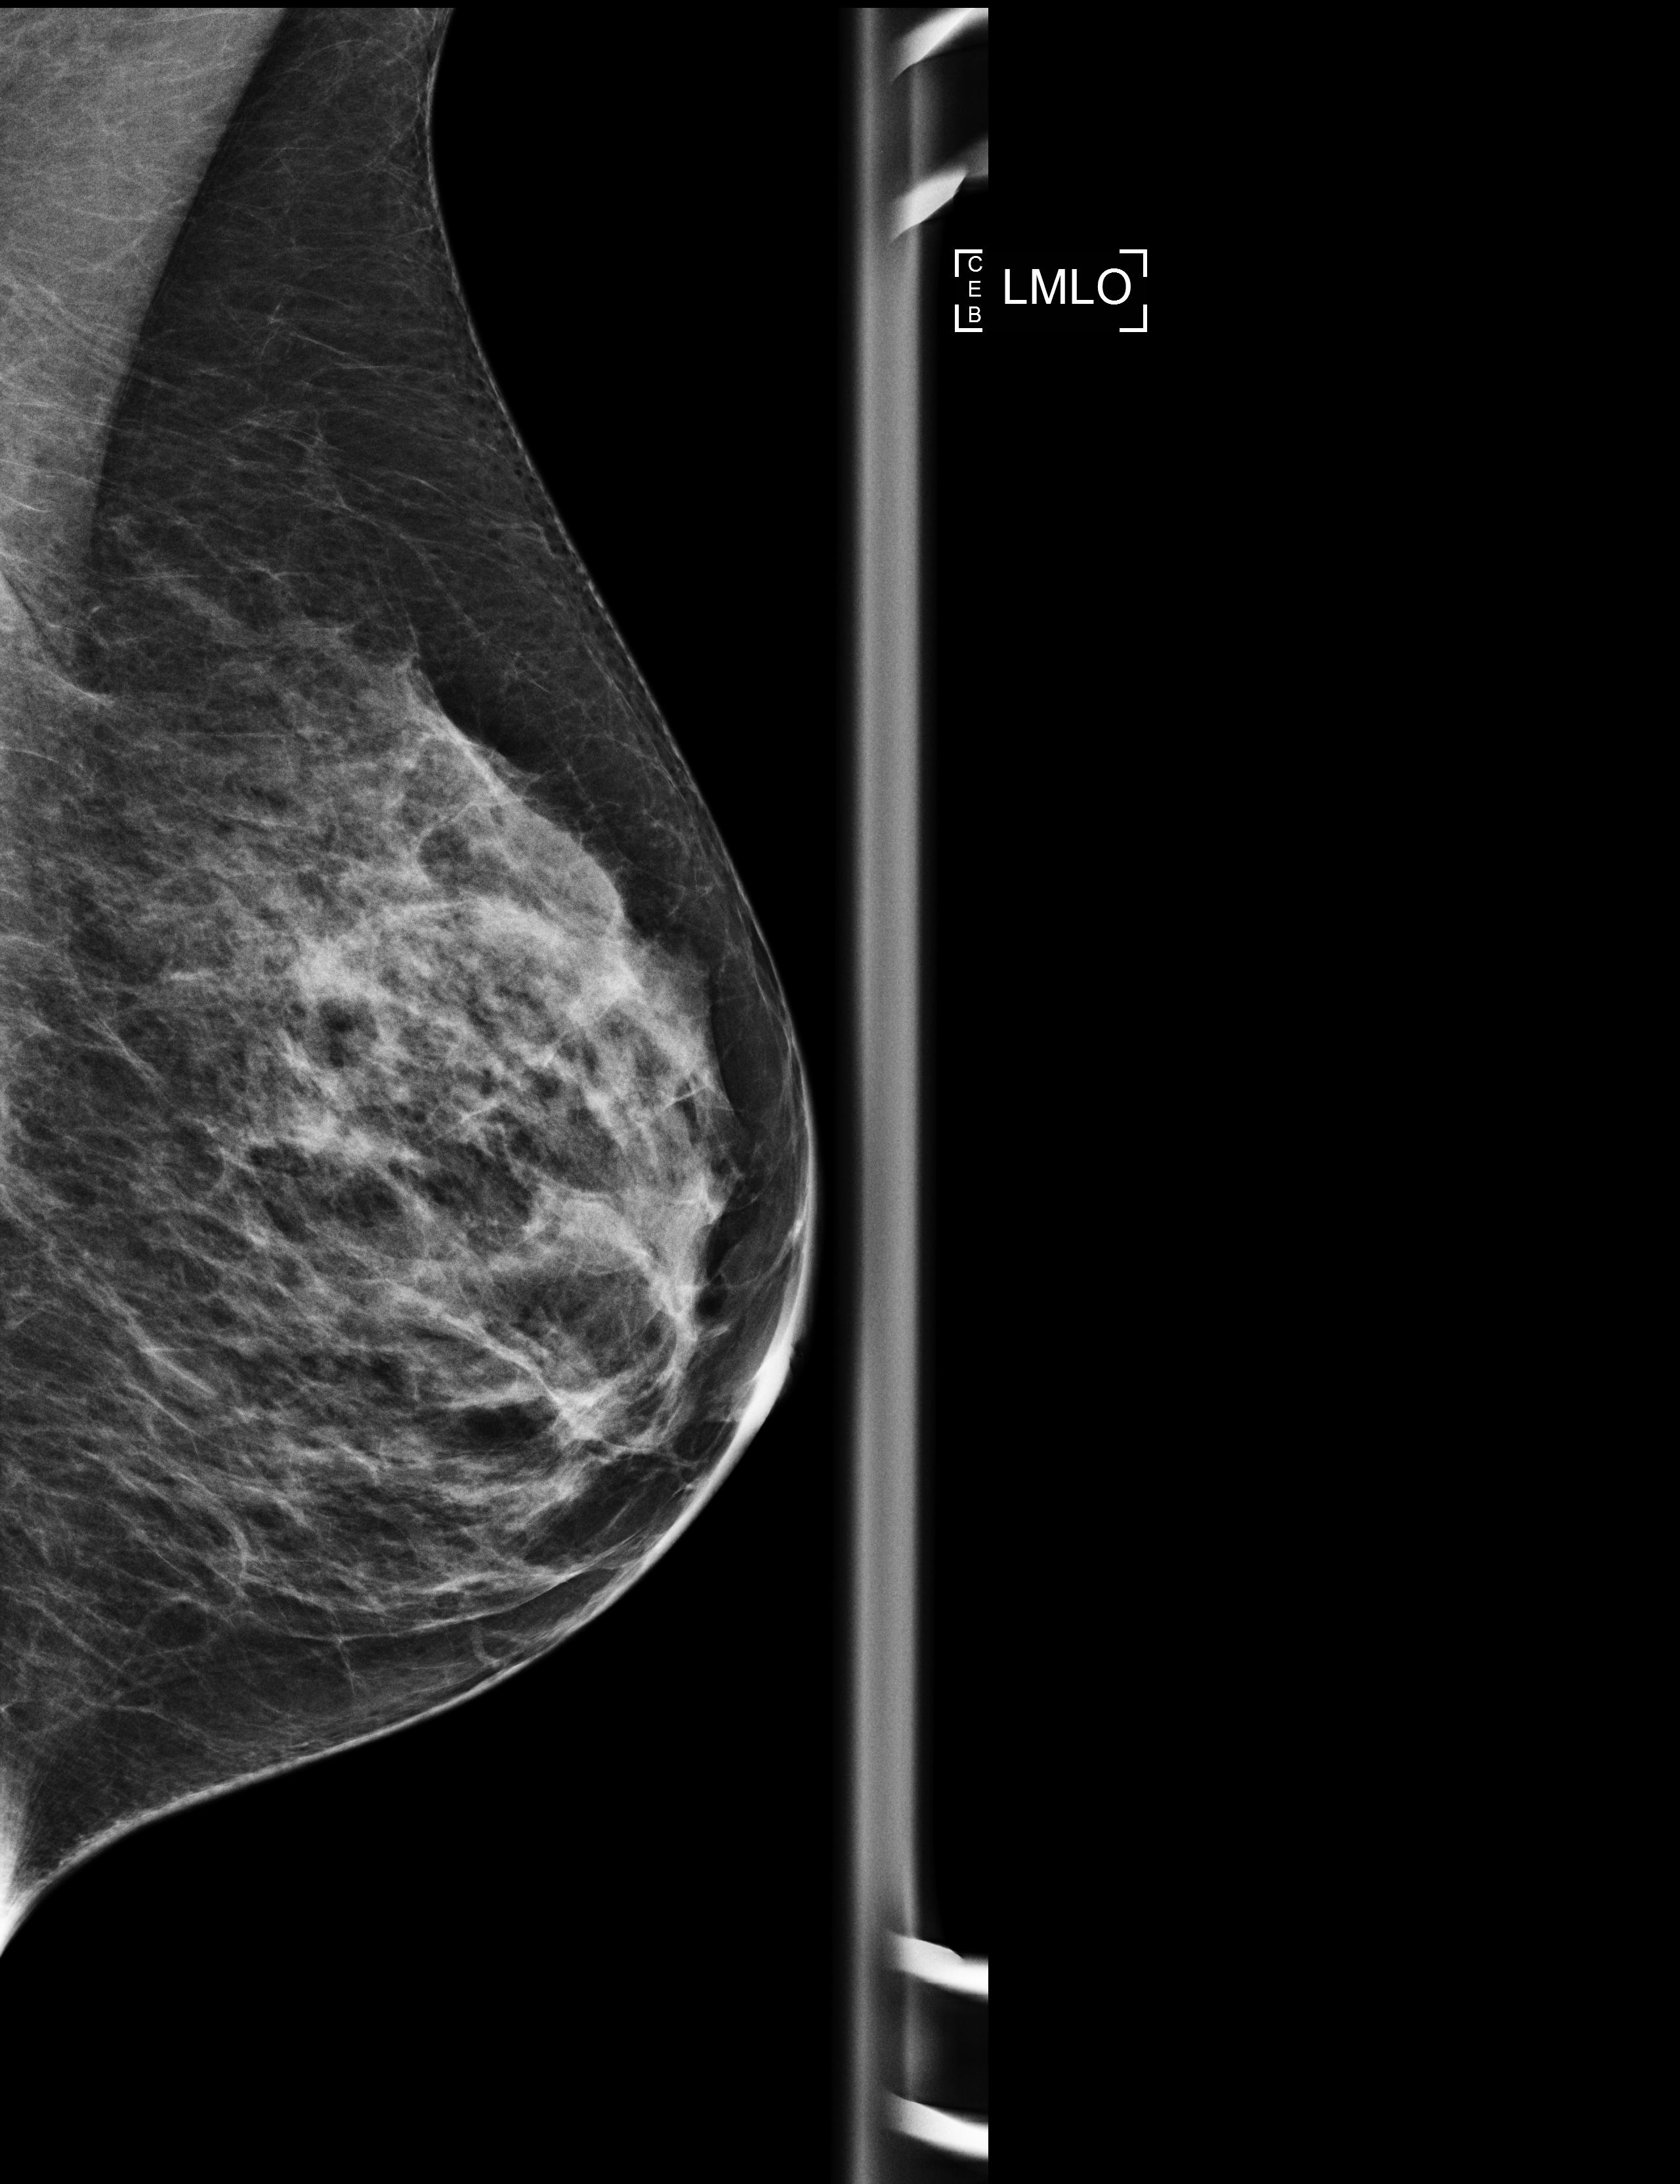
Digital mammogram (FFDM), left breast, medio-lateral oblique projection, annual screening mammography examination, compressed breast thickness 37 mm. Patient: female, 68 years.
BI-RADS breast density category at the screening exam (both breasts, scale 1–4): 3. Final BI-RADS assessment for this screening round (tomosynthesis exam, both breasts): category 2. Recall: no recall after this screen.